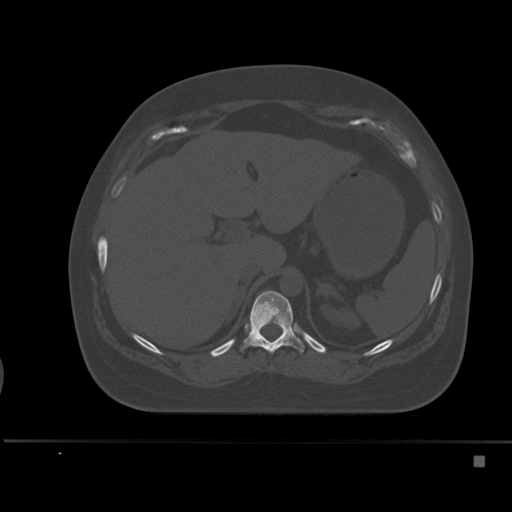
CT including the spine, one axial slice. Position 232 of 495 along the scan axis. Bone window (W 1800 / L 400 HU). 512 × 512 image matrix. Patient: female, 33 years. From the clinical record (not read from this slice): primary cancer: breast; vertebrae with lytic lesions (as recorded): T1.
Annotated regions visible in this slice (semi-automatically segmented with operator editing):
- T11 vertebra: box from (x=240, y=291) to (x=305, y=353) px